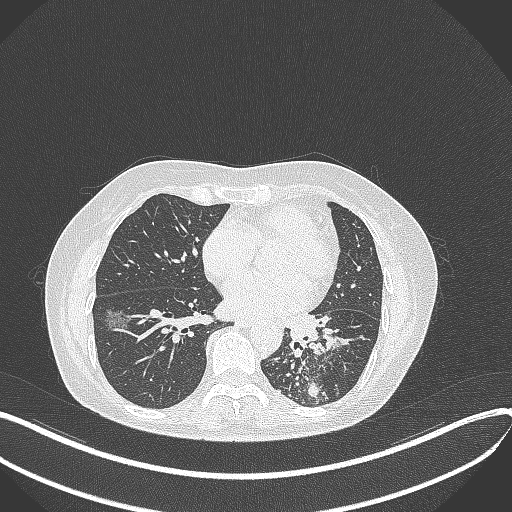
Chest CT, one axial slice. Position 170 of 429 along the scan axis. Reconstruction kernel B70f. 100 kVp. Lung window (W 1500 / L -600 HU). 1 mm slice thickness. 512 × 512 image matrix. Female patient, age 63 years. From the clinical record (not read from this slice): clinical TNM (as recorded): T1b N0 M0.
Annotated regions visible in this slice (bounding box drawn by a radiologist):
- lung tumour (recorded histology: adenocarcinoma): bounding box [x1, y1, x2, y2] px = [281, 305, 341, 360]